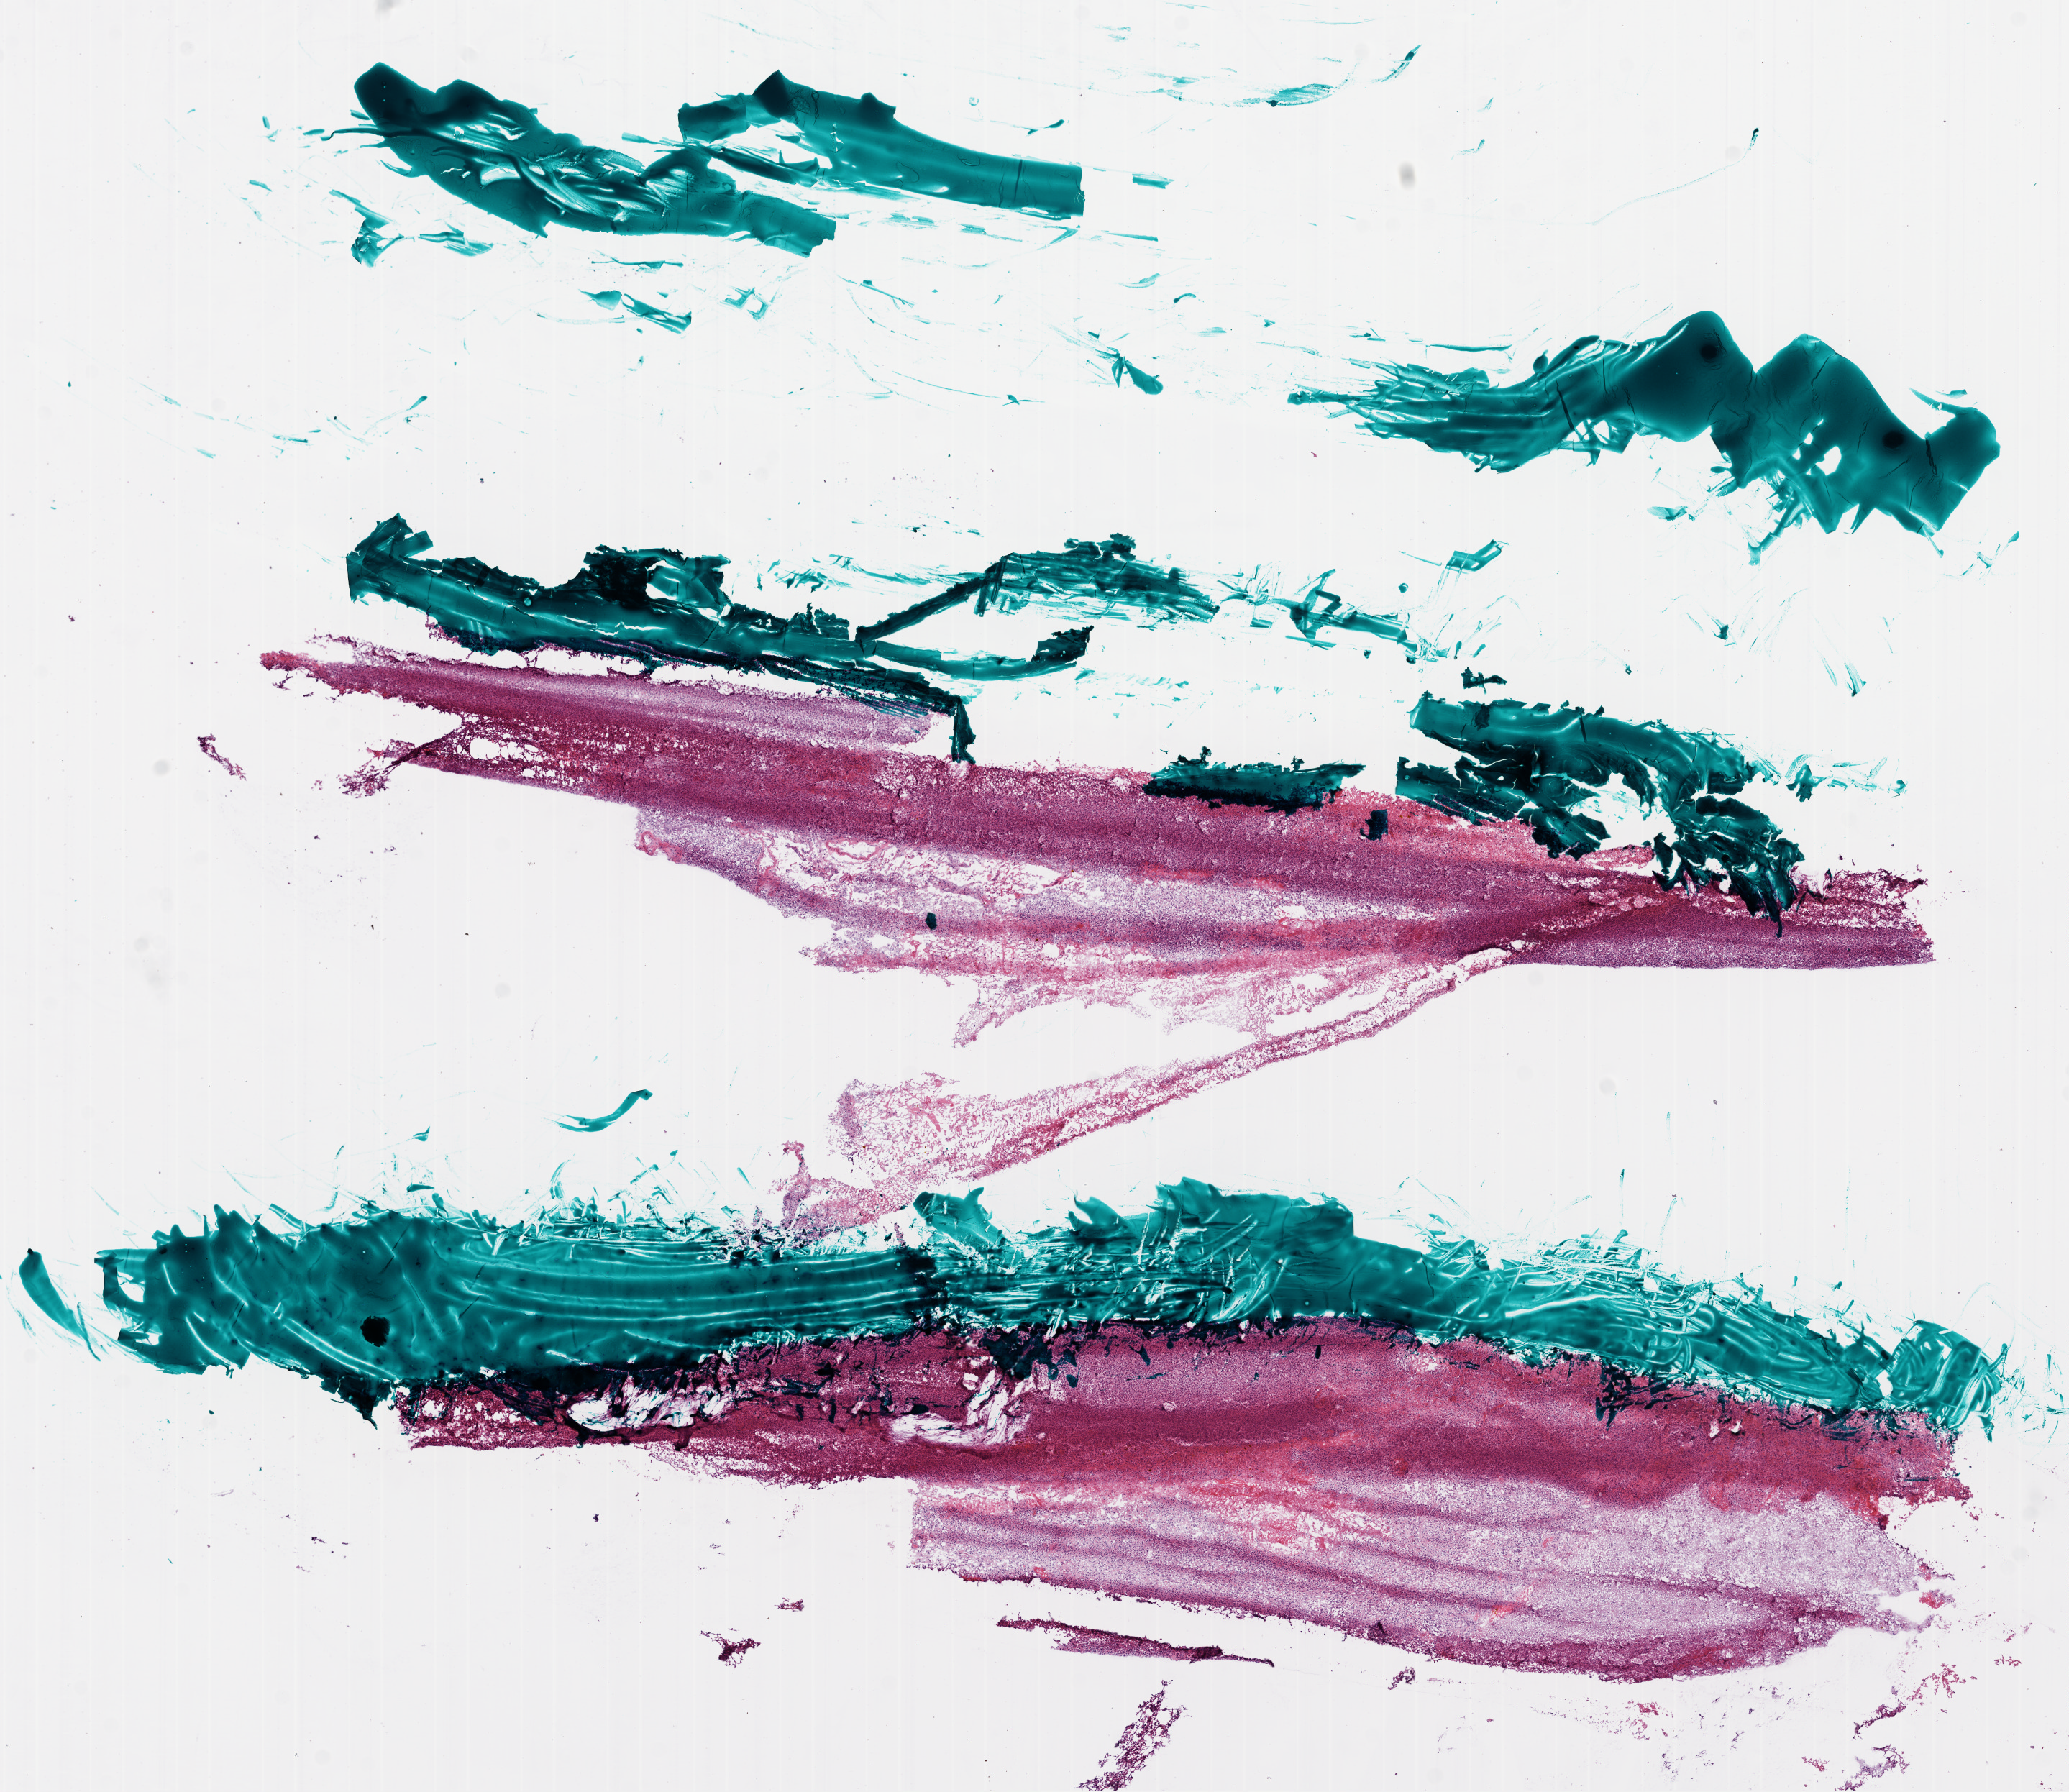
Hematoxylin and eosin (H&E) stained whole-slide image, a low-resolution overview of the entire scanned area, about 11.6 x 10.1 mm (slide scanned at 20x); frozen section from the bottom of the tissue portion; primary tumour sample from the brain. Patient: male, age at initial diagnosis 69 years. Pathologist review of this section (percent, as recorded): tumour cells 70%, tumour nuclei 95%, normal cells 0%, stromal cells 0%, necrosis 30%.
Diagnosis: Glioblastoma.